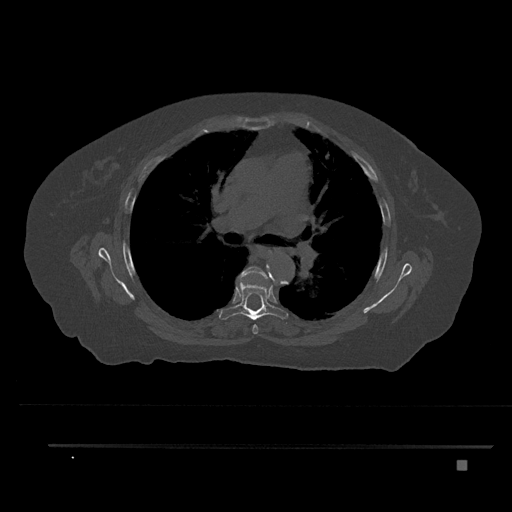
CT including the spine, one axial slice; position 537 of 797 along the scan axis; 120 kVp; bone window (W 1800 / L 400 HU); 0.5 mm slice thickness; 512 × 512 image matrix, field of view 437 × 437 mm. Patient: female, 76 years. Case-level facts recorded for this patient, not image findings: primary cancer: lung; vertebrae with lytic lesions (as recorded): T11, L3.
Outlined on this slice (semi-automatic segmentation, software-assisted and operator-edited):
- T5 vertebra: bounding box [x1, y1, x2, y2] px = [237, 266, 269, 334]
- T6 vertebra: [219, 275, 289, 320]